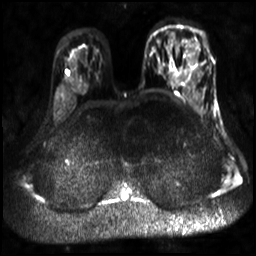
Breast MRI, one axial slice. Position 20 of 30 along the scan axis. Diffusion-weighted series; image 2 of 4 stored at this slice position (different b-values; order by instance number). 3 T. 4 mm slice thickness. 256 × 256 image matrix. Female patient.
Structures marked on this image (outlined manually by an expert reader):
- tumour on diffusion-weighted imaging: bounding box (x1, y1, x2, y2) in pixels: (185, 41, 203, 74)